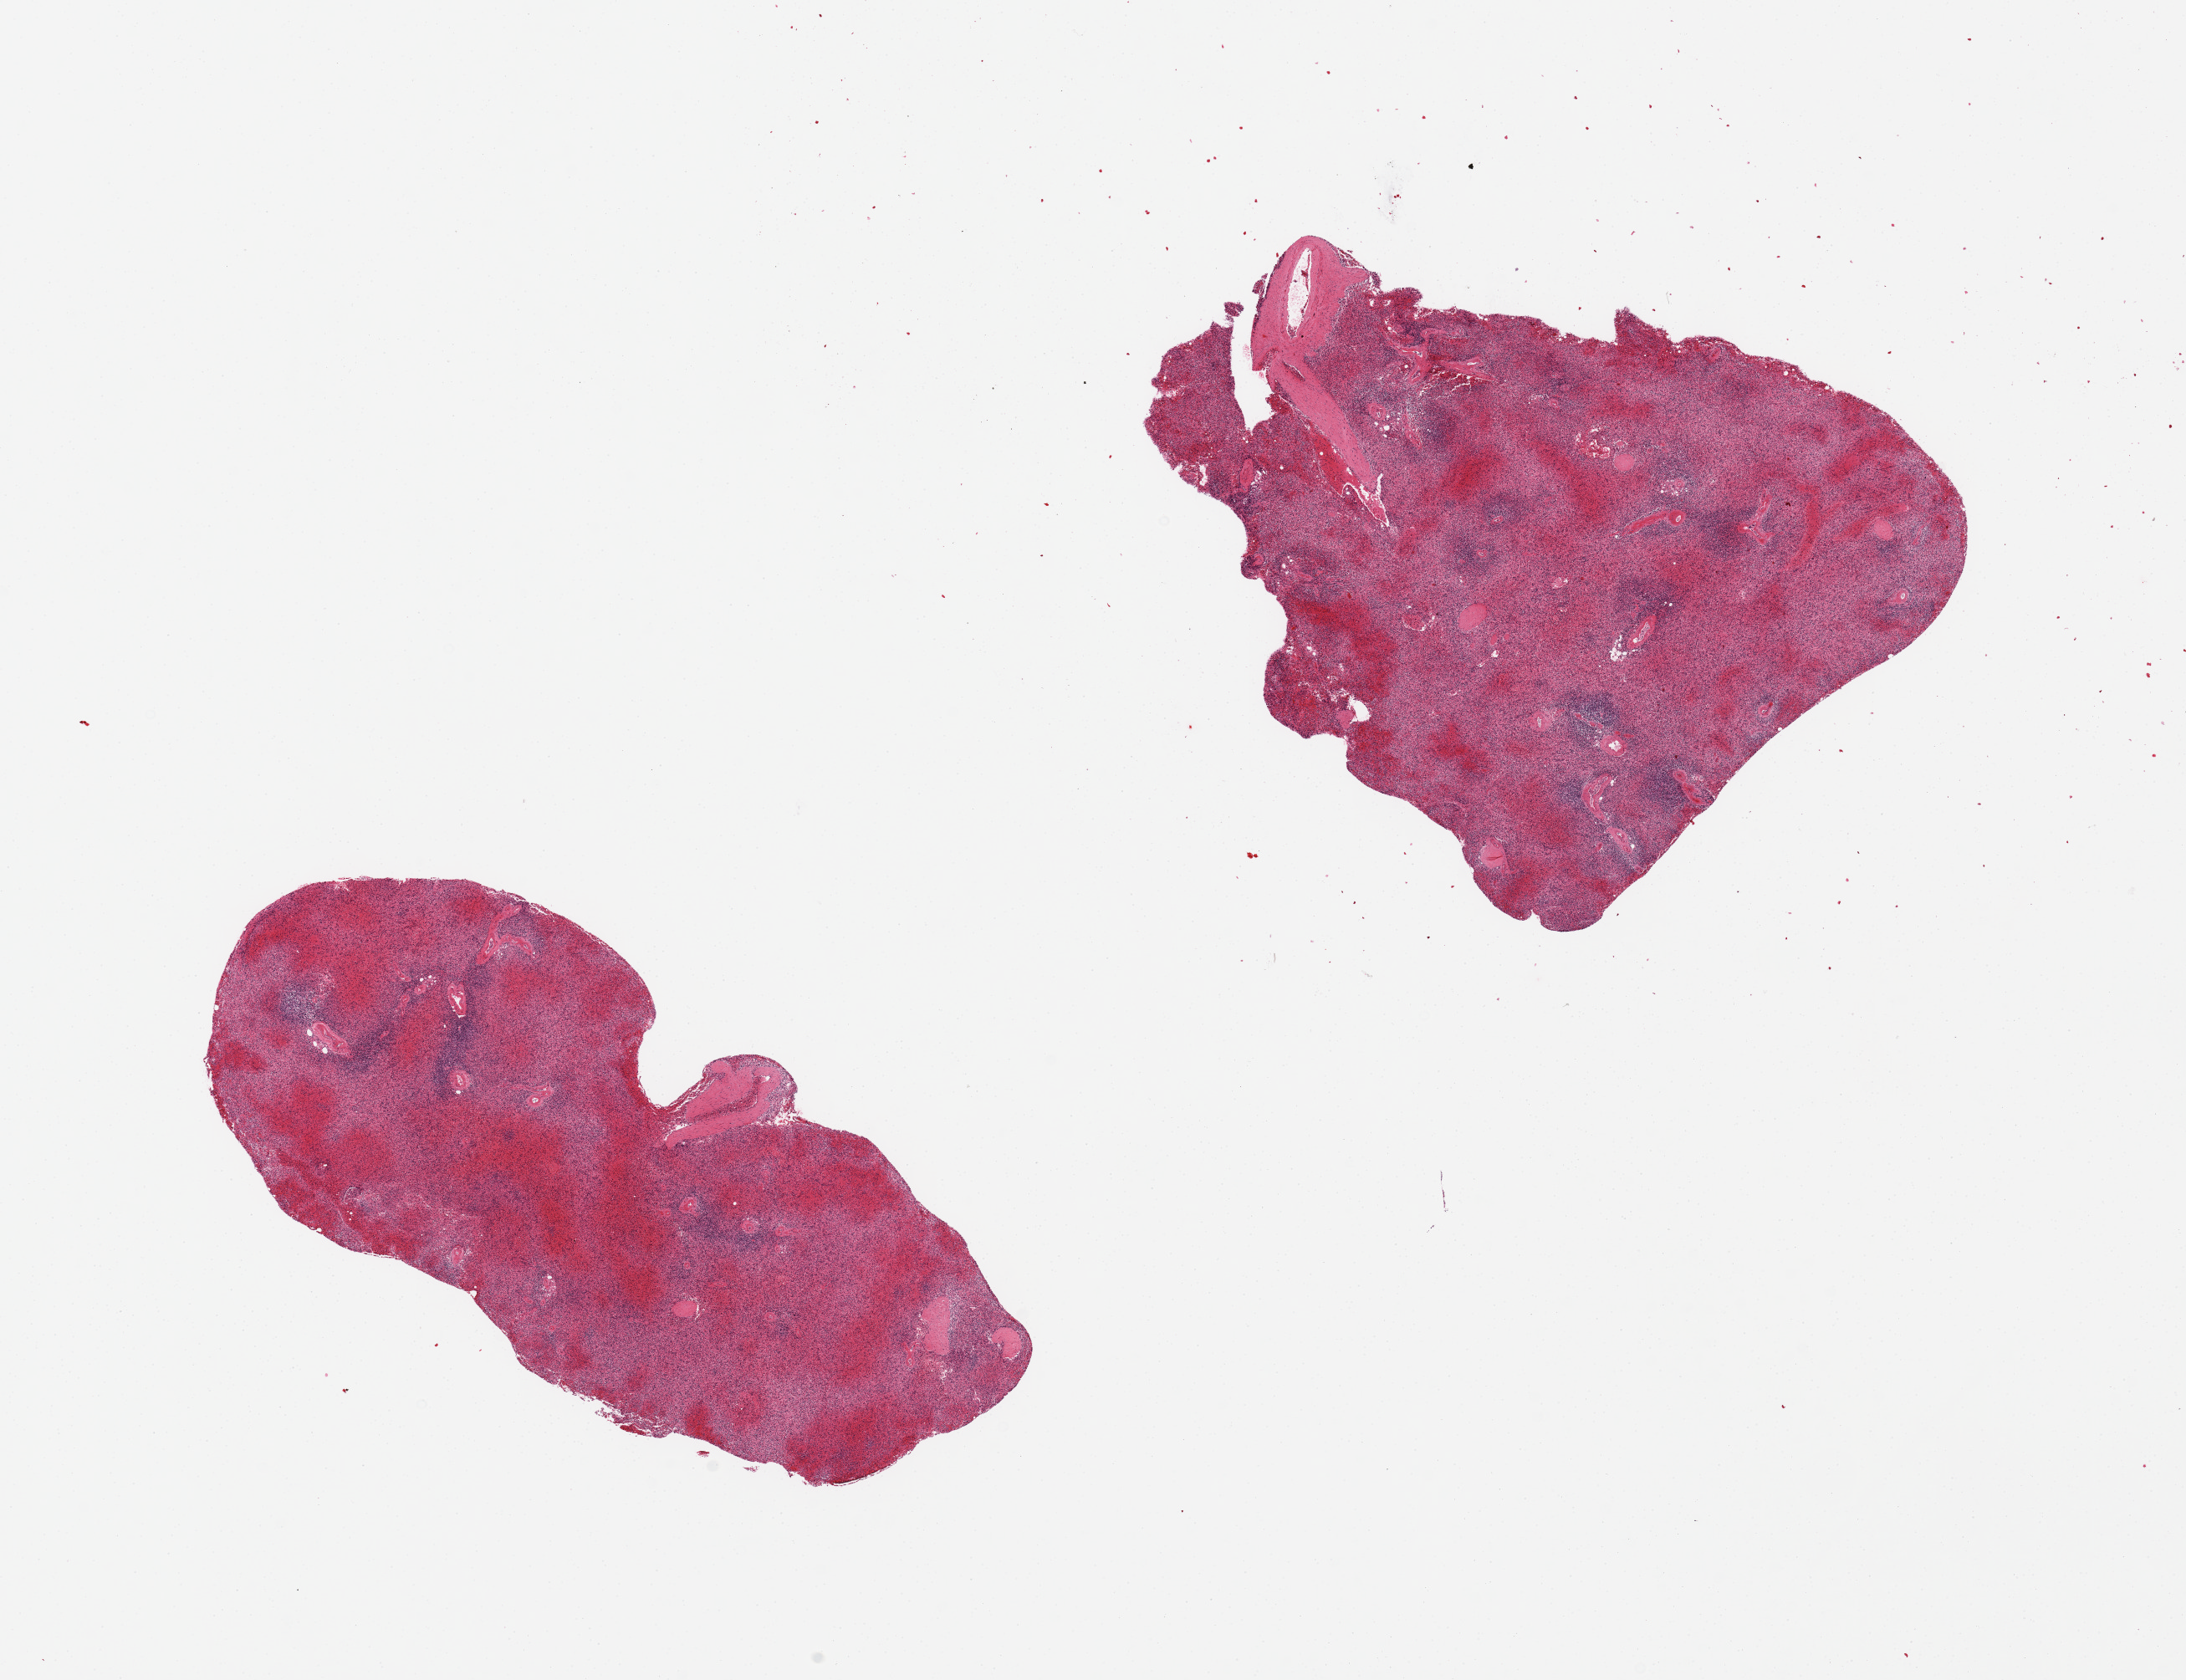
Whole-slide image, H&E stain, whole scanned area (about 20.7 x 15.9 mm) shown as a low-resolution overview. PAXgene-fixed paraffin-embedded (PFPE) section. Section of spleen (target tissue). Tissue donor sample. Male donor.
• review note (as recorded): 2 pieces, moderate congestion